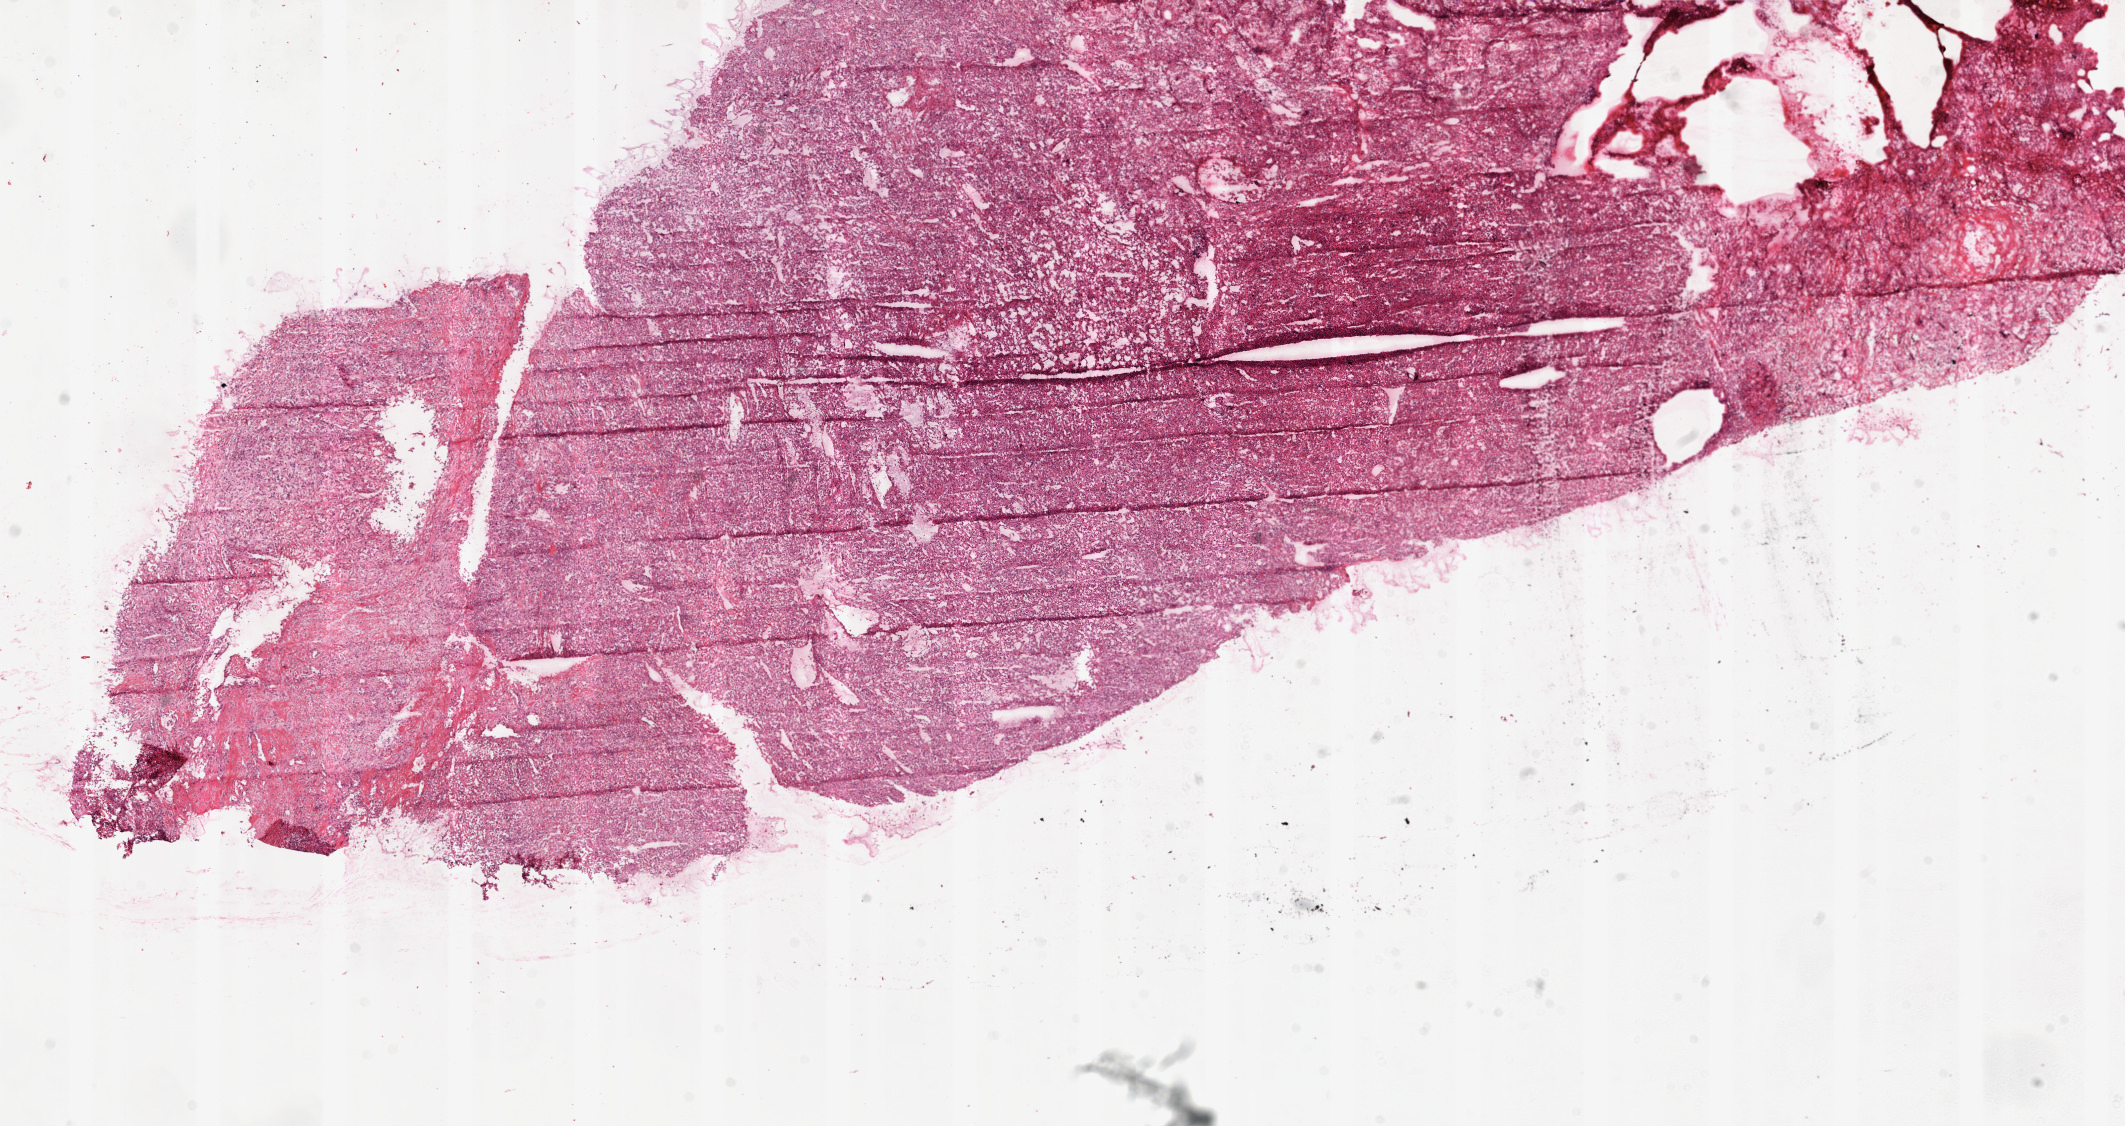
Digitized H&E-stained tissue section (whole slide) — shown as a low-resolution overview of the whole scanned area (about 17.1 x 9.0 mm); frozen section; primary tumour sample from the kidney. Female patient; age at initial diagnosis 53 years. Histologic grade: G3 (poorly differentiated). Slide review estimates, as recorded: tumour cells 90%, tumour nuclei 85%, normal cells 0%, stromal cells 10%, necrosis 0%.
• diagnosis: Clear cell adenocarcinoma, NOS
• laterality: left
• TNM: T1a N0 M1
• AJCC pathologic stage: IV